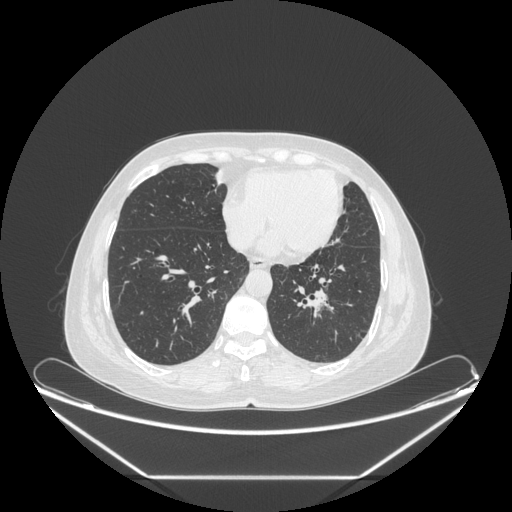
Chest CT, one axial slice. Slice 86 of 241 in the series (ordered by position). Reconstruction kernel STANDARD. 120 kVp. Lung window (W 1500 / L -600 HU). 1.25 mm slice thickness. 512 × 512 image matrix, field of view 451 × 451 mm. Female patient, age 63 years. Case-level facts recorded for this patient, not image findings: clinical TNM (as recorded): T1c N0 M0; histopathological grade: G2-3.
Outlined on this slice (bounding box drawn by a radiologist):
- lung tumour (recorded histology: adenocarcinoma): bounding box [x1, y1, x2, y2] px = [299, 283, 340, 334]